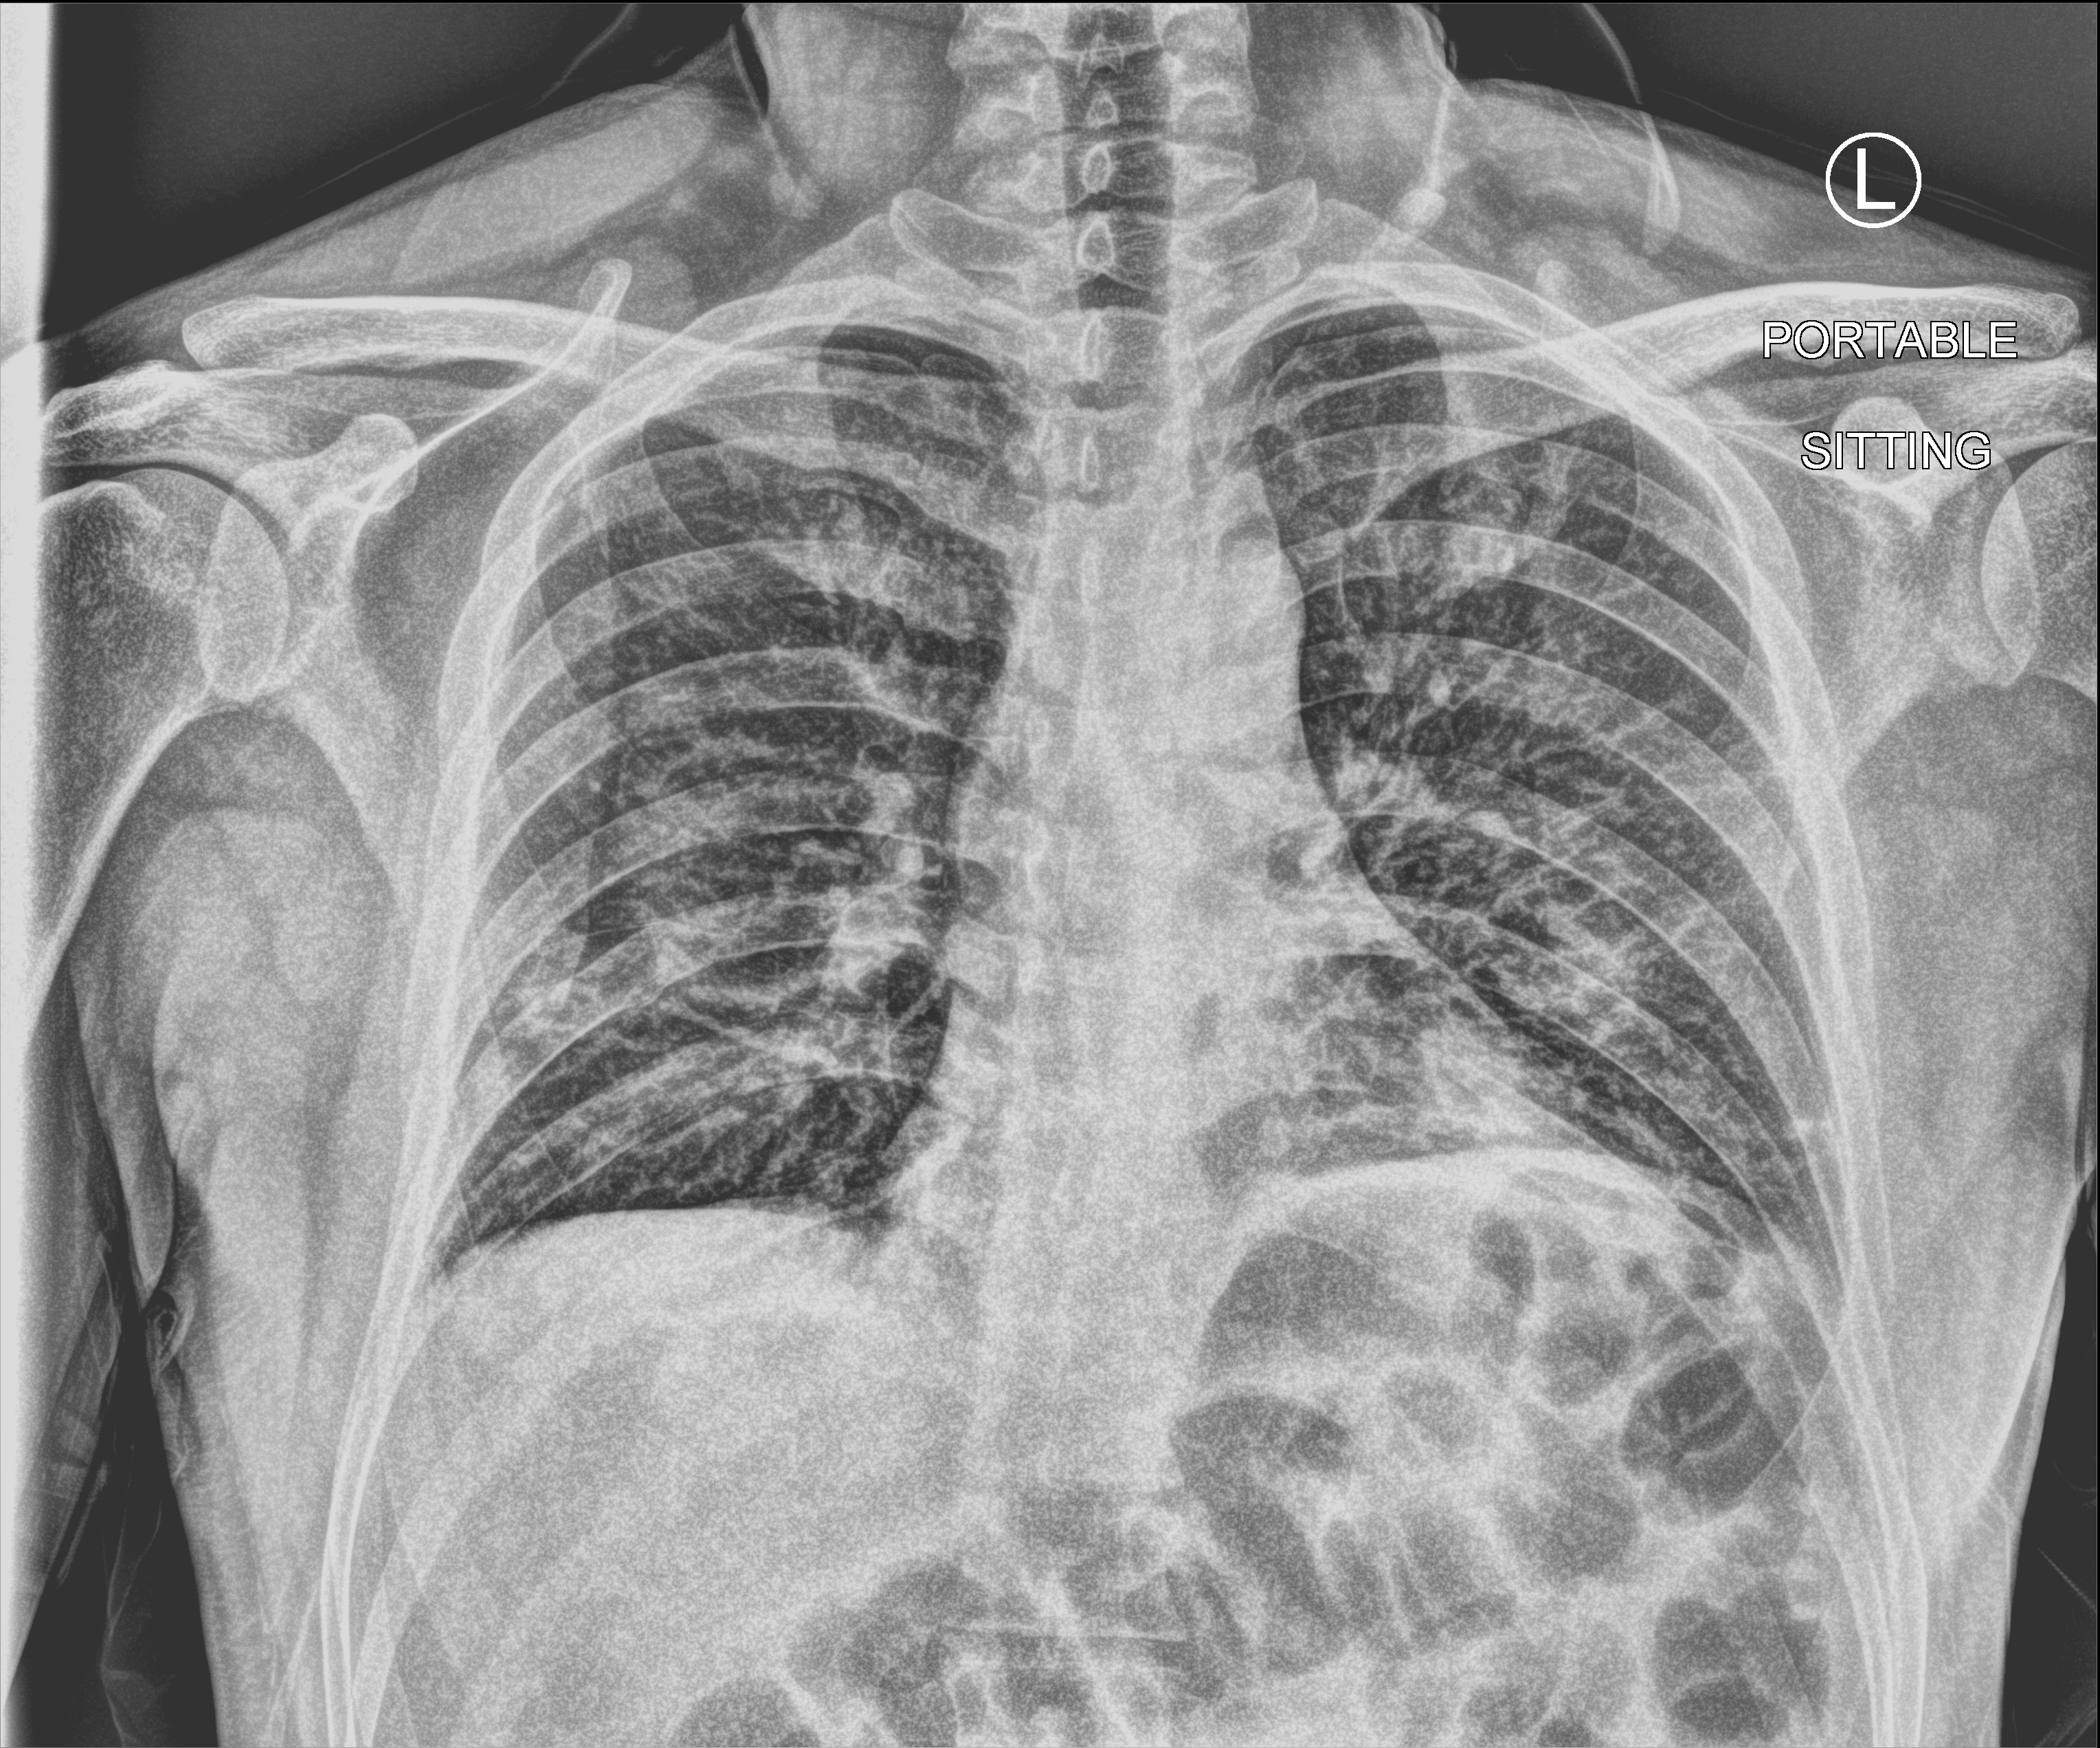
Portable chest radiograph, anteroposterior (AP) projection. Patient hospitalised with COVID-19; male, aged 18–59 years.
Hospital-stay facts (about this admission, not read from this image; timing relative to this image not recorded):
- mechanically ventilated during this hospital stay: no
- hypertension (admission record): no
- length of hospital stay: 1 day